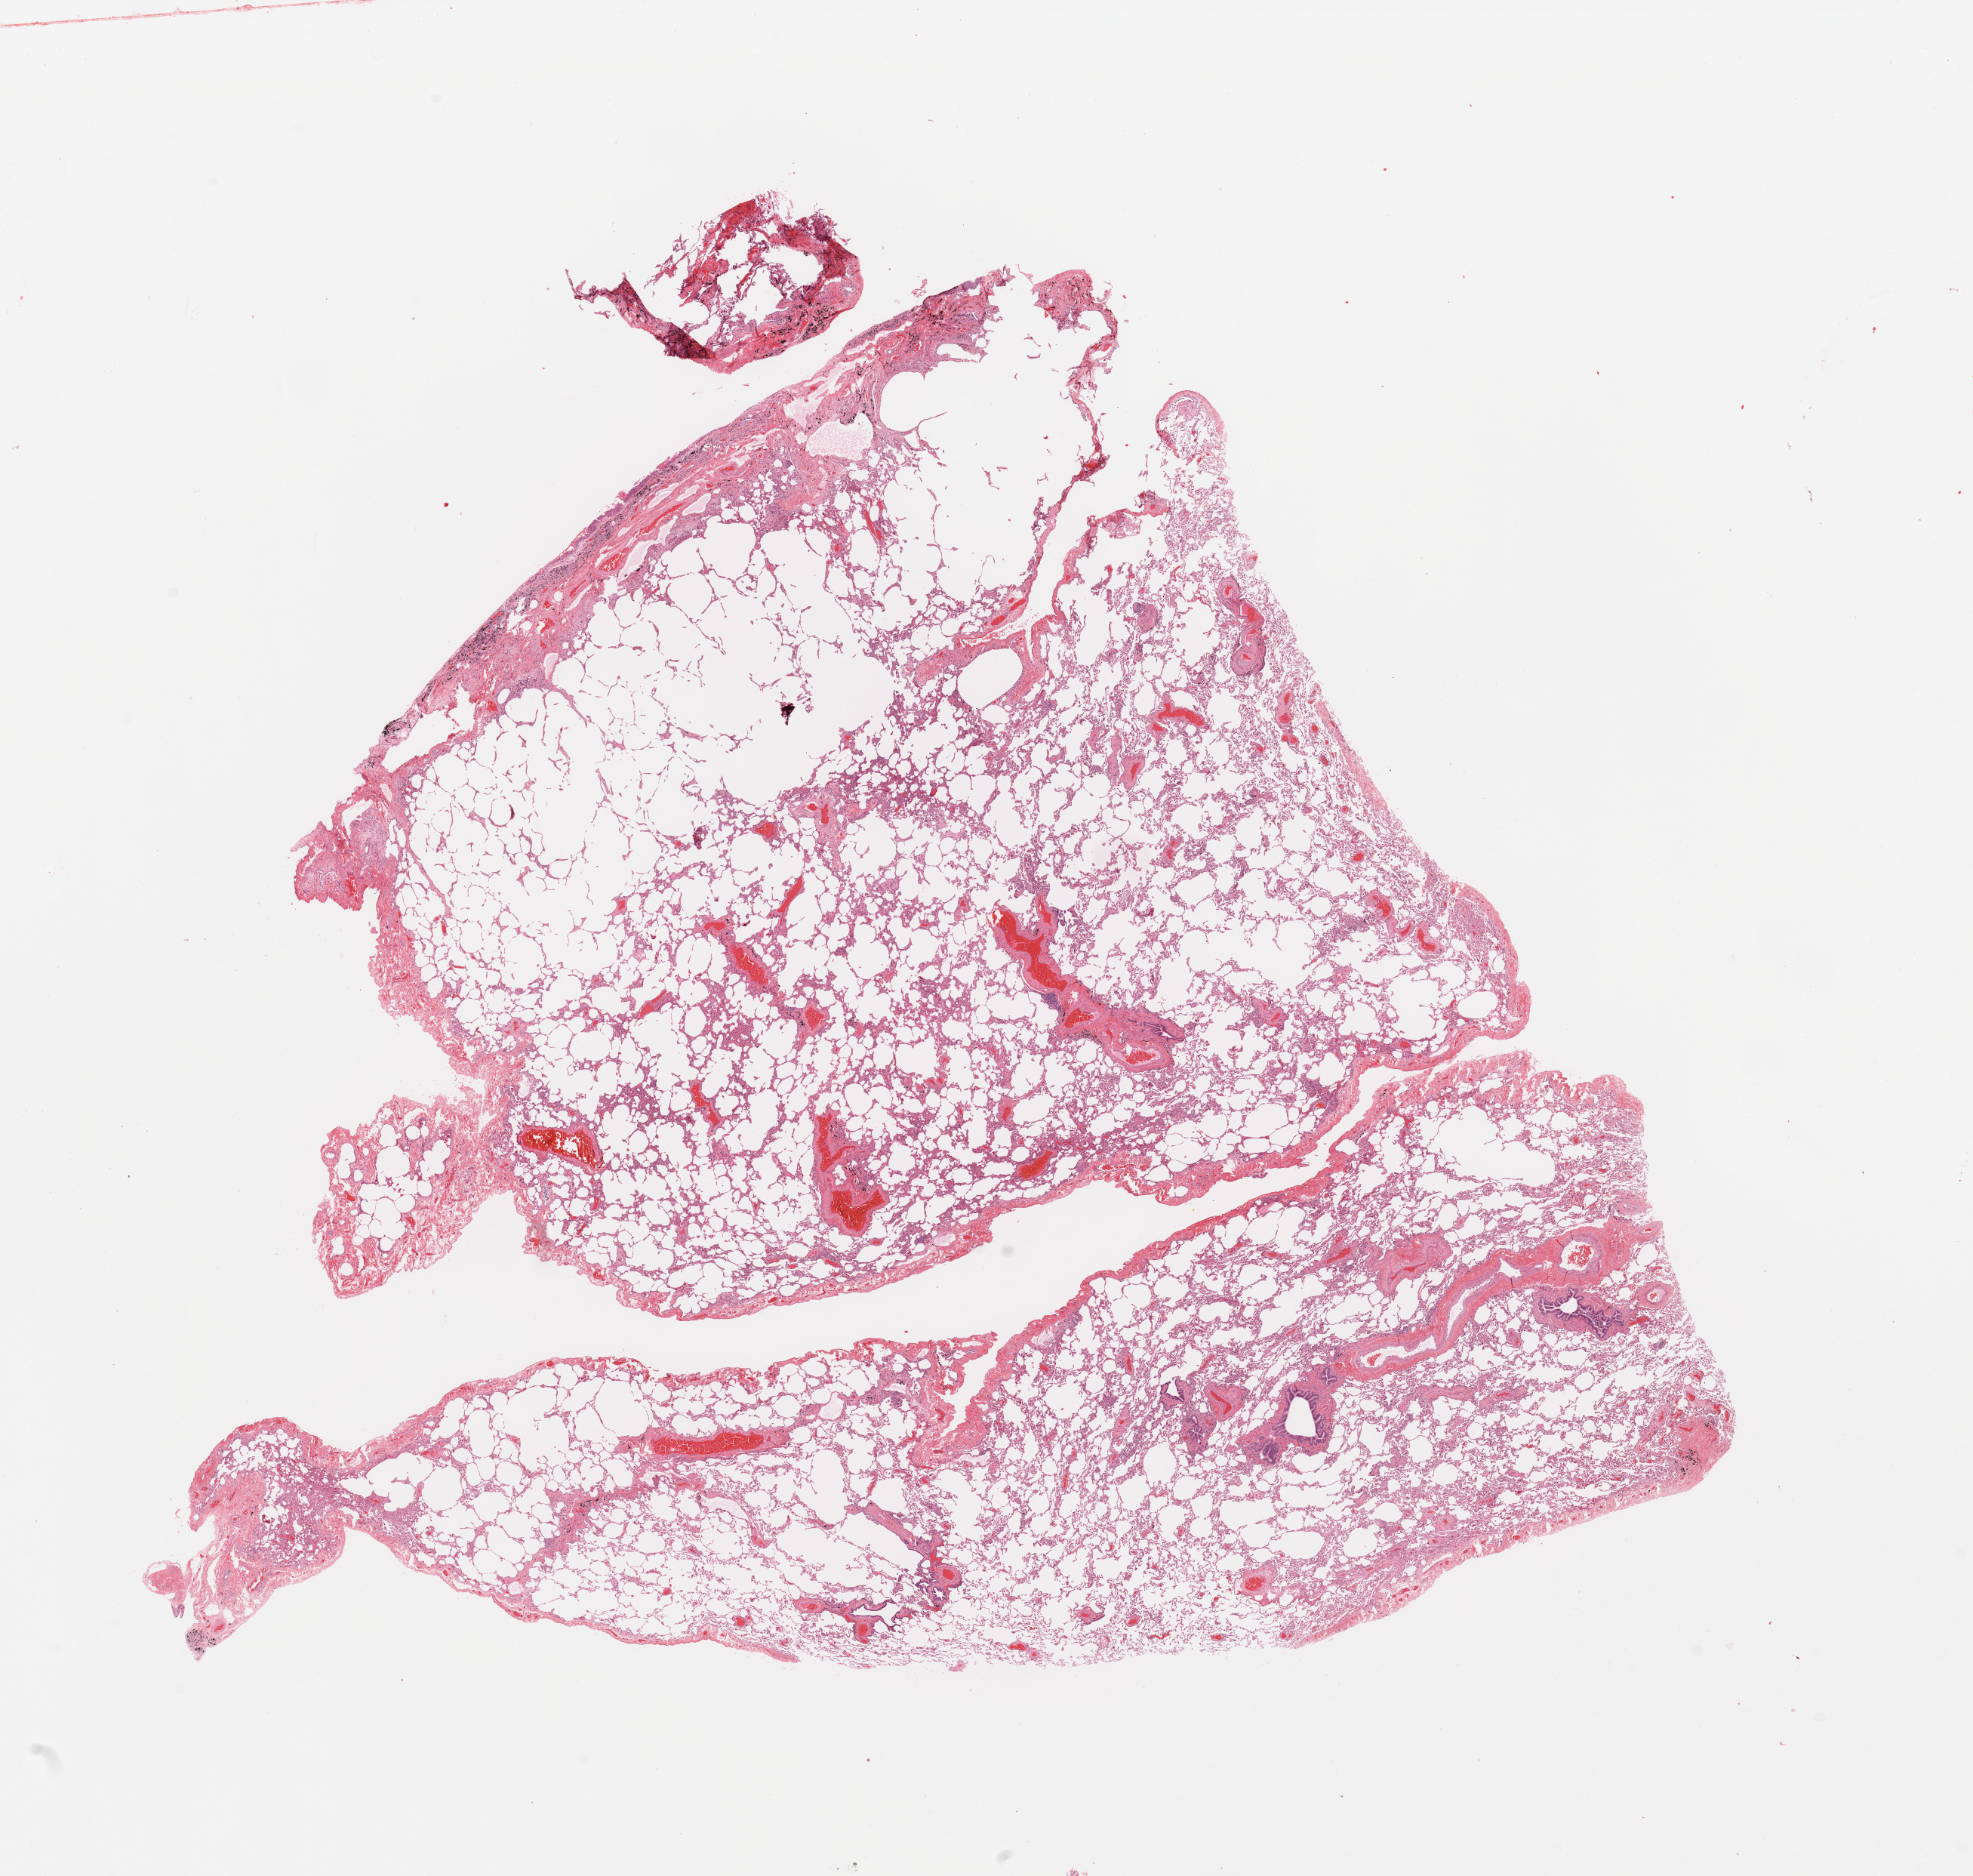
Digitized H&E-stained tissue section (whole slide), shown as a low-resolution overview of the whole scanned area (about 20.7 x 19.7 mm, from a 20x scan). Normal (non-tumour) tissue sample, sampled site: lung. Male, 69 y/o.
- this section: normal (non-tumour) tissue from the same patient
- patient diagnosis: Adenocarcinoma, NOS